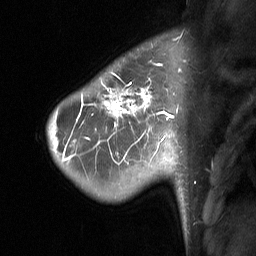
Breast MRI (dynamic contrast-enhanced), one sagittal slice. Slice 52 of 64 in the series (ordered by position). Dynamic contrast-enhanced study with each time point stored as its own series, time point 2 of 3 at this slice position (early post-contrast, ordered by acquisition time). 1.5 T. TE 4.8 ms, TR 27 ms. 2 mm slice thickness. 256 × 256 image matrix. Patient: female, 42 years. Case-level facts recorded for this patient, not image findings: setting: breast cancer imaged before/during neoadjuvant chemotherapy; receptor status: triple-negative.
Outlined on this slice (semi-automatically segmented with operator editing):
- analysis volume of interest (the breast-tissue region the enhancement analysis was run in; not a lesion): bounding box [x1, y1, x2, y2] px = [49, 45, 196, 197]
- tumour enhancement mask (voxels above the 90 % enhancement threshold inside the analysis volume of interest): [53, 82, 174, 151]